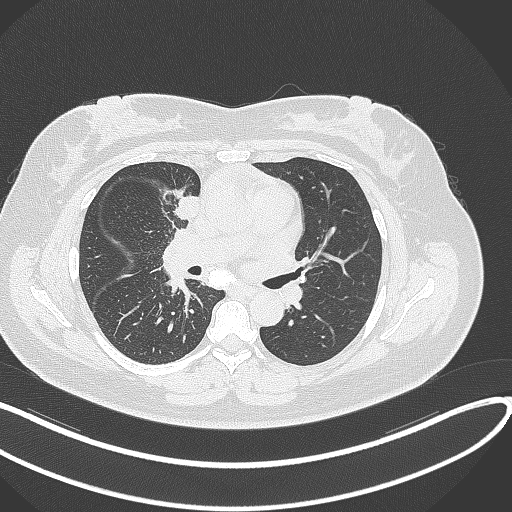
Chest CT, one axial slice; slice 149 of 303 in the series (ordered by position); reconstruction kernel B70f; 120 kVp; lung window (W 1500 / L -600 HU); 1 mm slice thickness; 512 × 512 image matrix, field of view 400 × 400 mm. Patient: female, 46 years. From the clinical record (not read from this slice): clinical TNM (as recorded): T2a N1 M0.
Annotated regions visible in this slice (rectangle marked by the reading radiologist):
- lung tumour (recorded histology: adenocarcinoma): bounding box [x1, y1, x2, y2] px = [171, 189, 204, 225]